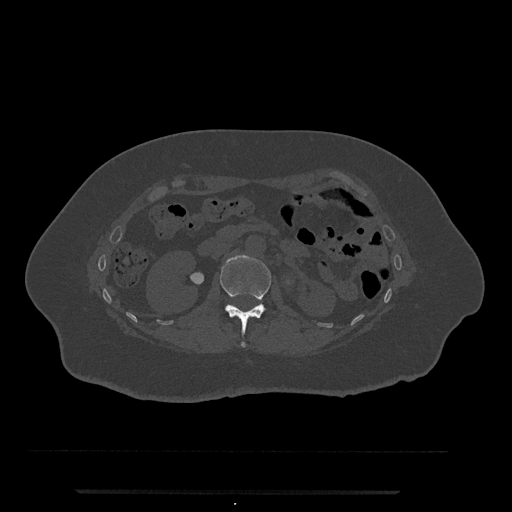
CT including the spine, one axial slice. Position 97 of 797 along the scan axis. Reconstruction kernel Br40s/3. Bone window (W 1800 / L 400 HU). 0.5 mm slice thickness. 512 × 512 image matrix, field of view 440 × 440 mm. Female patient, age 51 years. Case-level facts recorded for this patient, not image findings: primary cancer: neuro.
Annotated regions visible in this slice (semi-automatic segmentation, software-assisted and operator-edited):
- L1 vertebra: bounding box [x1, y1, x2, y2] px = [220, 255, 271, 347]